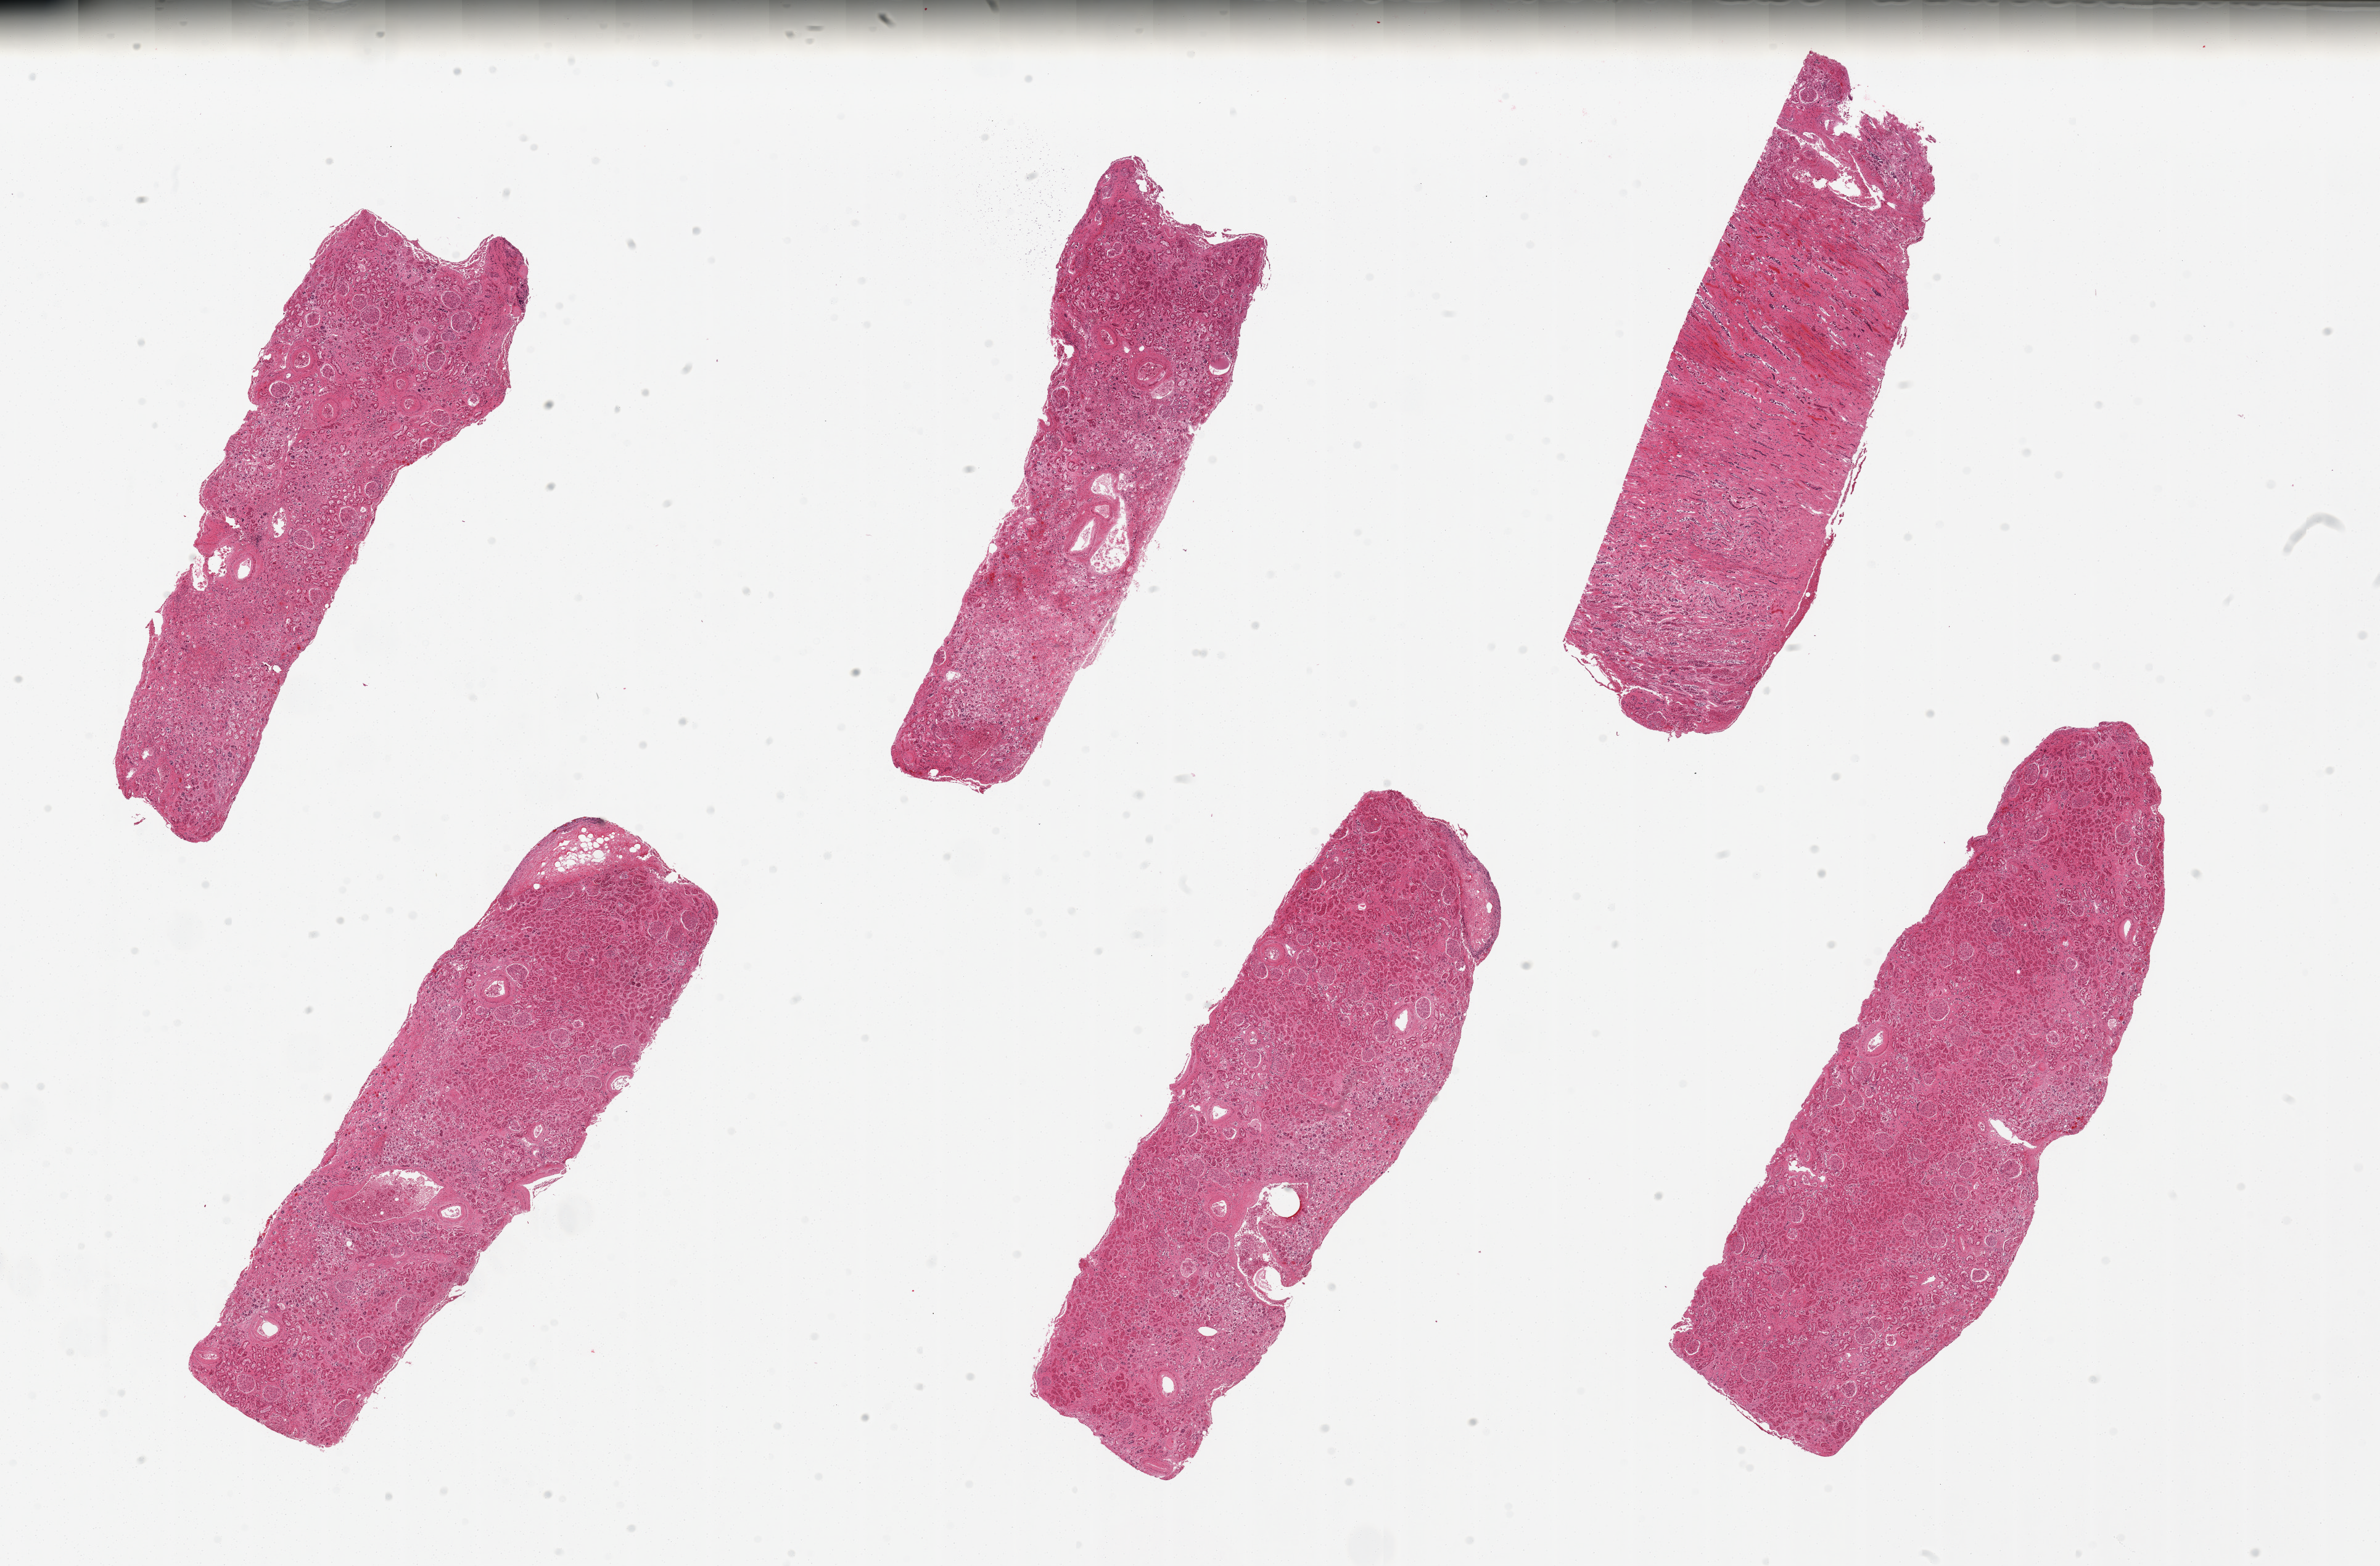
Digitized hematoxylin and eosin (H&E)-stained section, brightfield, a low-resolution overview of the entire scanned area, about 30.5 x 20.1 mm (from a 20x scan); PAXgene-fixed paraffin-embedded (PFPE) section; target tissue: renal cortex; donor tissue sample. Male donor.
Reviewer comment on this tissue sample: 6 pieces, glomeruli present, one is largely medullary rays, but all sections badly autolyzed.